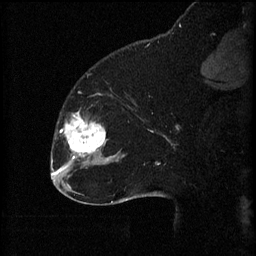
Breast MRI (dynamic contrast-enhanced), one sagittal slice. Position 19 of 60 along the scan axis. 3 images stored at this slice position (order not interpretable as contrast timing). 1.5 T. TE 4.2 ms, TR 8.2 ms. 2 mm slice thickness. 256 × 256 image matrix. Female patient, age 32 years.
Structures marked on this image (semi-automatic segmentation, software-assisted and operator-edited):
- analysis volume of interest (the breast-tissue region the enhancement analysis was run in; not a lesion): bounding box (x1, y1, x2, y2) in pixels: (59, 112, 111, 165)
- tumour enhancement mask (voxels above the 70 % enhancement threshold inside the analysis volume of interest): (65, 112, 106, 159)